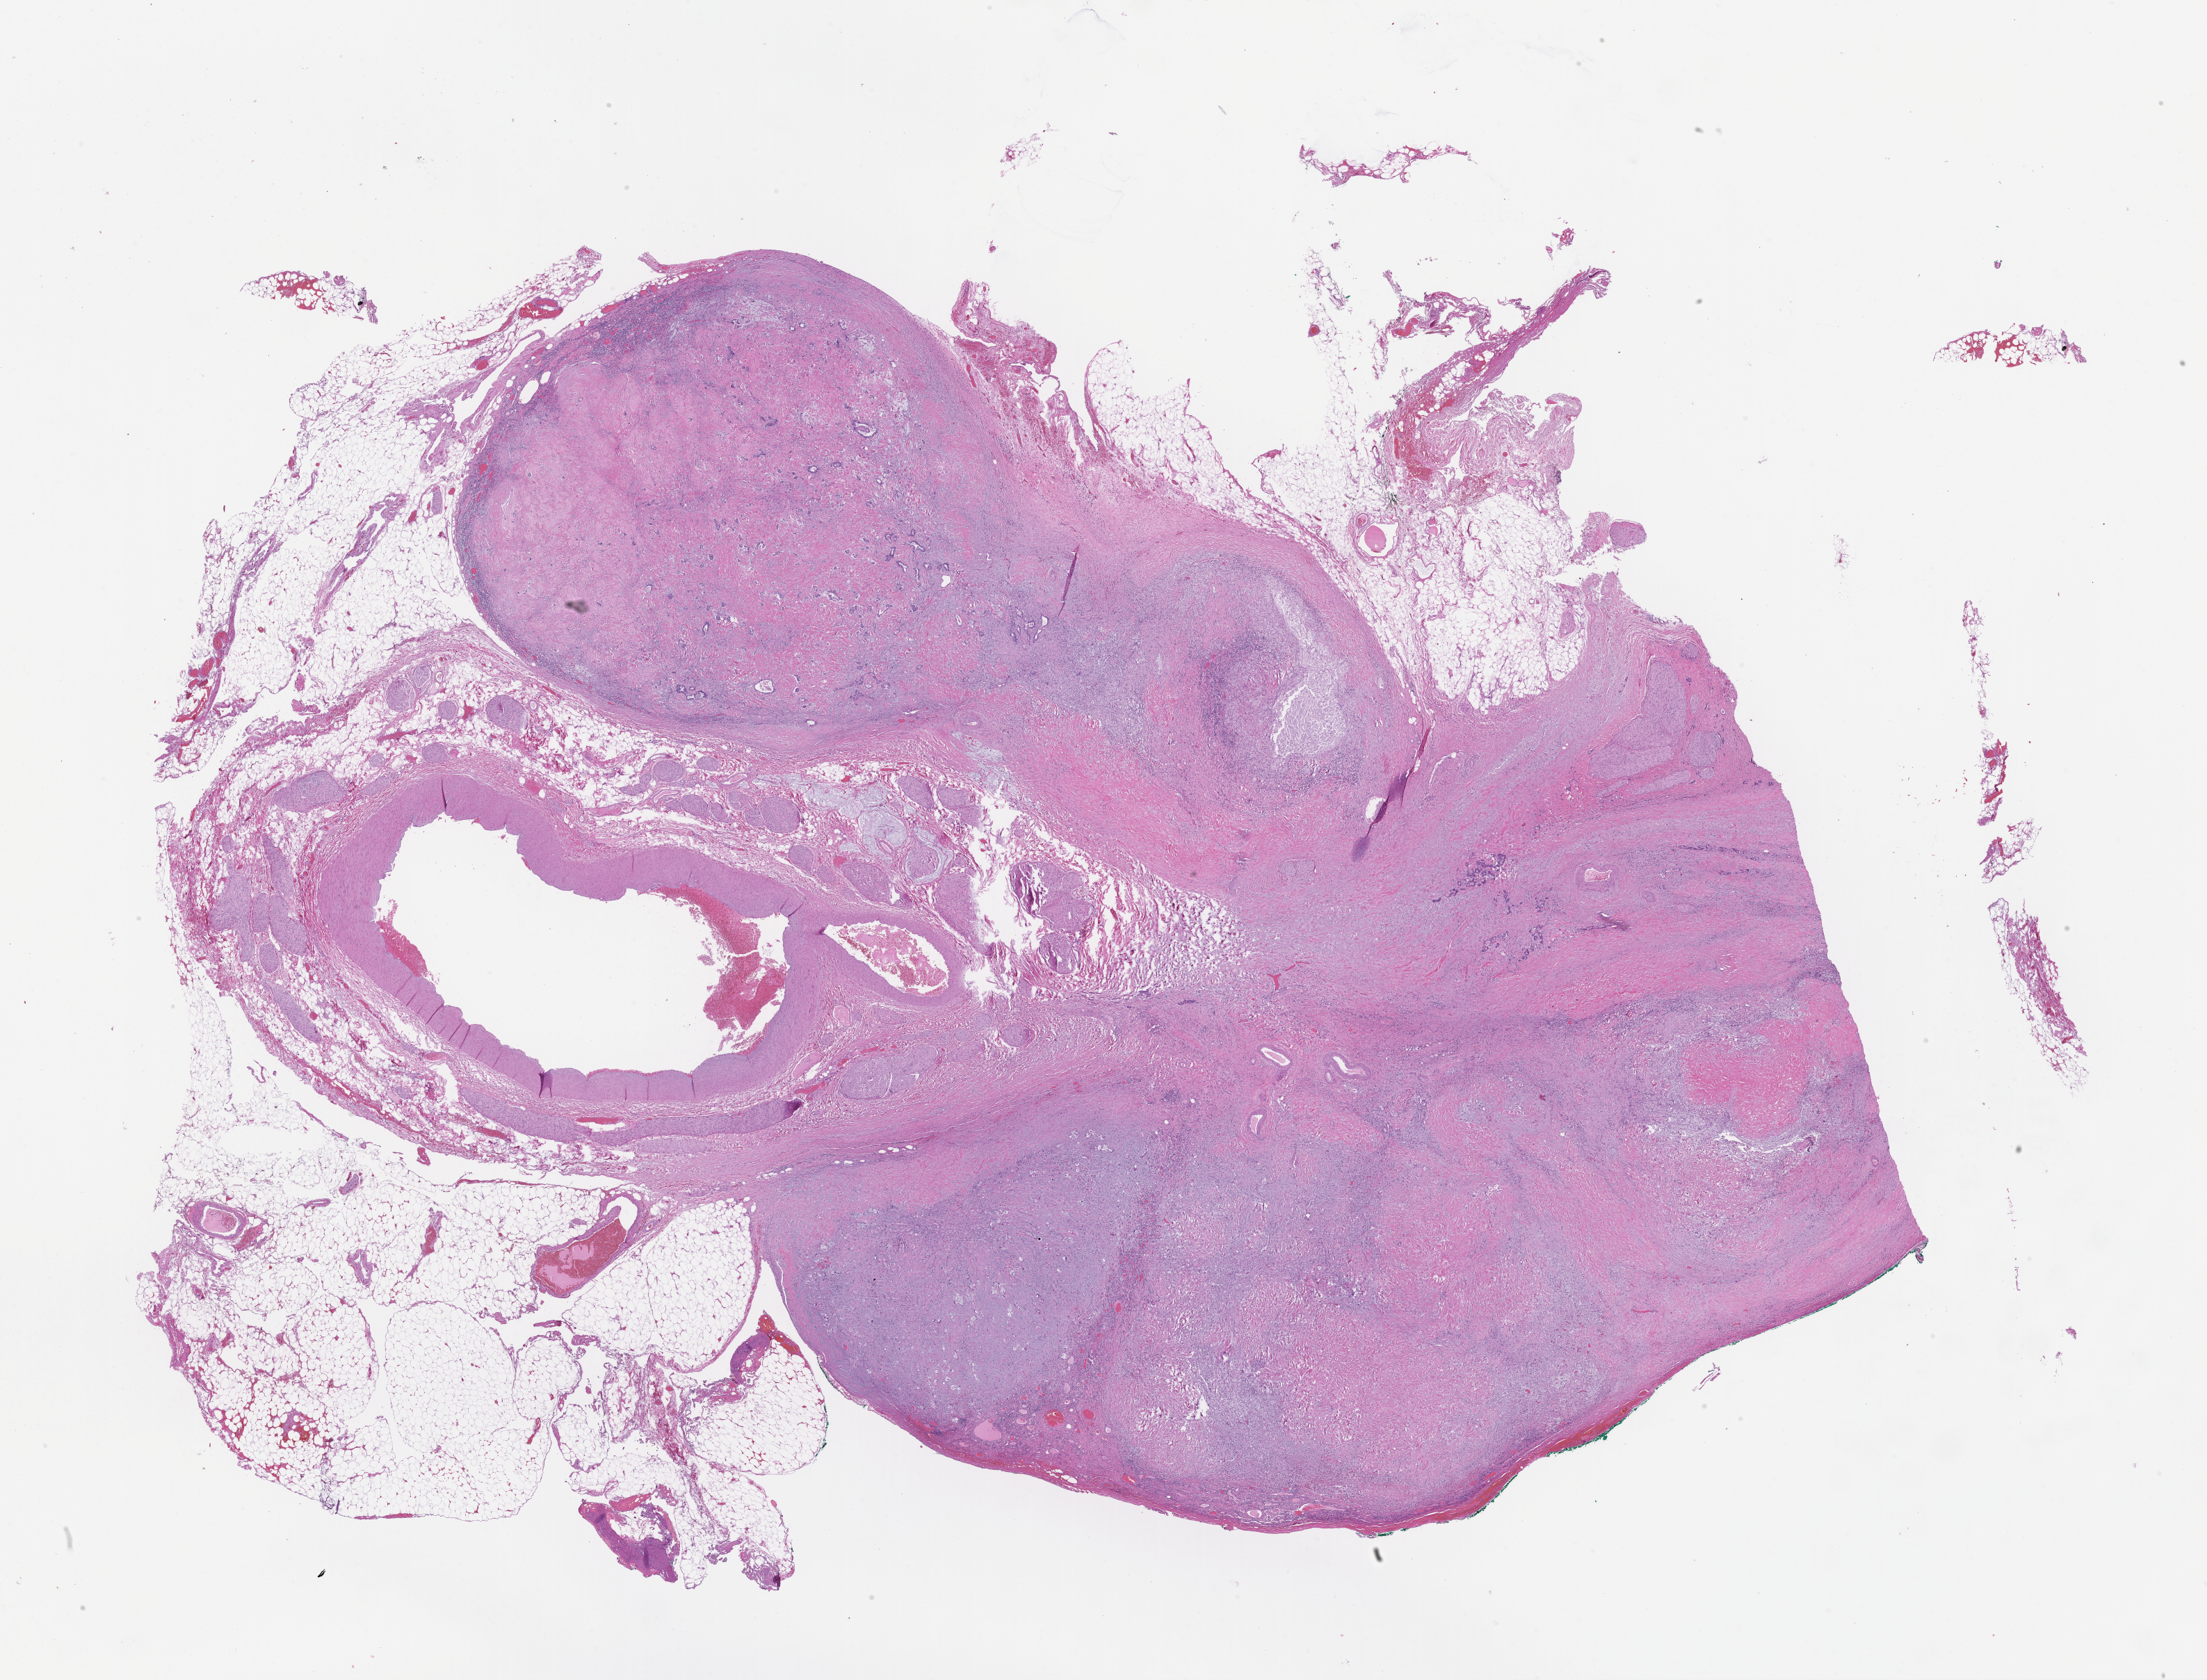
Digitized hematoxylin and eosin (H&E)-stained section, a low-resolution overview of the entire scanned area, about 25.6 x 19.5 mm. Formalin-fixed, paraffin-embedded (FFPE) tissue. Specimen time point: archival tissue. Patient sex: male.
This section: metastatic tumor tissue. Primary diagnosis of the patient: Adenocarcinoma of the Gastroesophageal Junction.